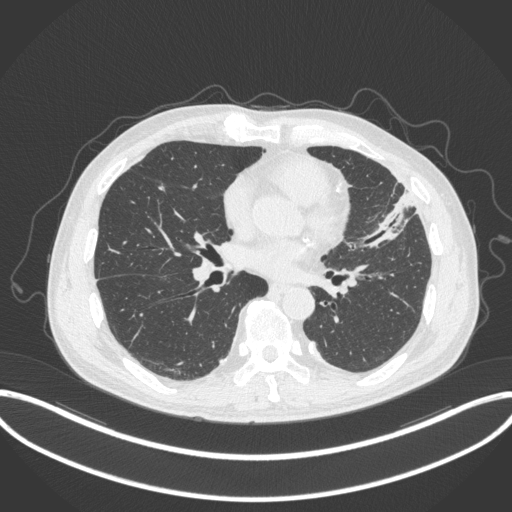
Chest CT, one axial slice; position 153 of 382 along the scan axis; 120 kVp; lung window (W 1500 / L -600 HU); 1 mm slice thickness; 512 × 512 image matrix. Male patient, age 64 years. Case-level facts recorded for this patient, not image findings: clinical TNM (as recorded): T4 N1 M0; histopathological grade: G3.
Structures marked on this image (rectangle marked by the reading radiologist):
- lung tumour (recorded histology: adenocarcinoma): box from (x=360, y=189) to (x=419, y=251) px